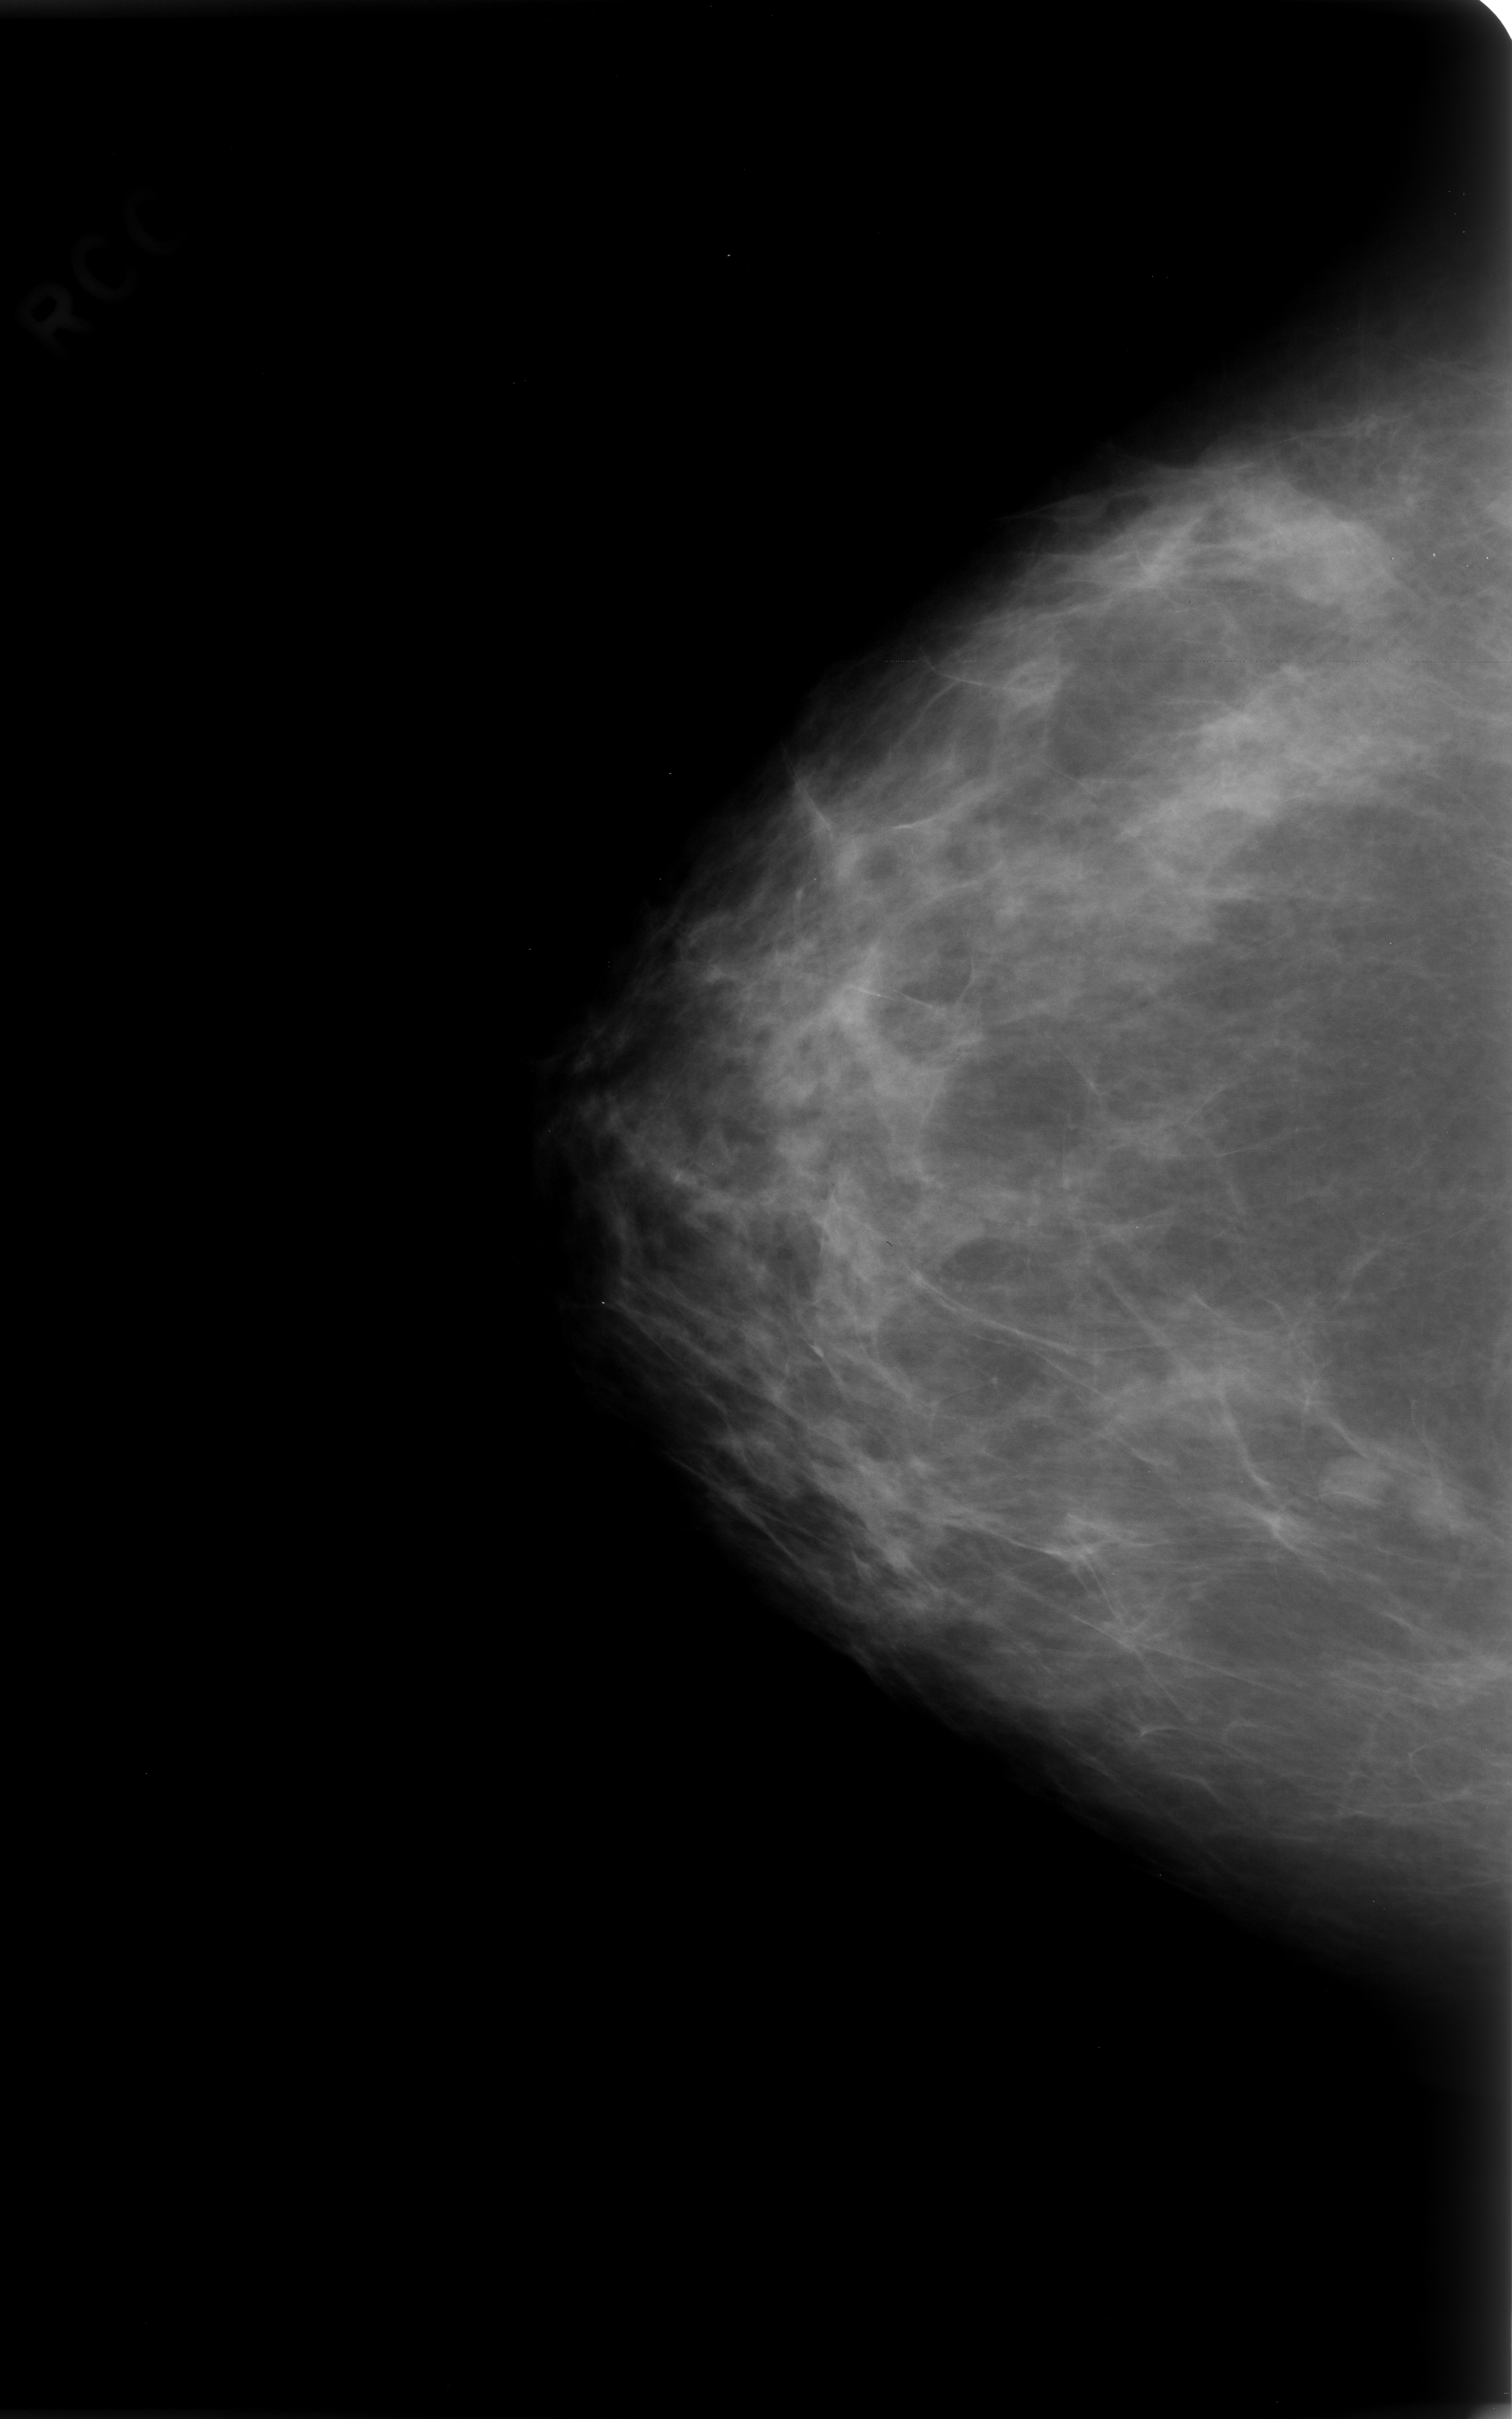
Digitized screen-film mammogram; right breast; craniocaudal (CC) view; breast composition: scattered fibroglandular densities (BI-RADS density category 2 of 4).
Abnormality record for this image: Finding 1 of 3: mass, shape lobulated, margins circumscribed; BI-RADS assessment category 3; pathology (as recorded): benign. Finding 2 of 3: mass, shape oval, margins circumscribed; BI-RADS assessment category 3; pathology result (as recorded, not read from the image): benign. Finding 3 of 3: mass, shape round, margins circumscribed; BI-RADS assessment category 3; subtlety rating 5 on a 1 (subtle) to 5 (obvious) scale; pathology (as recorded): benign.